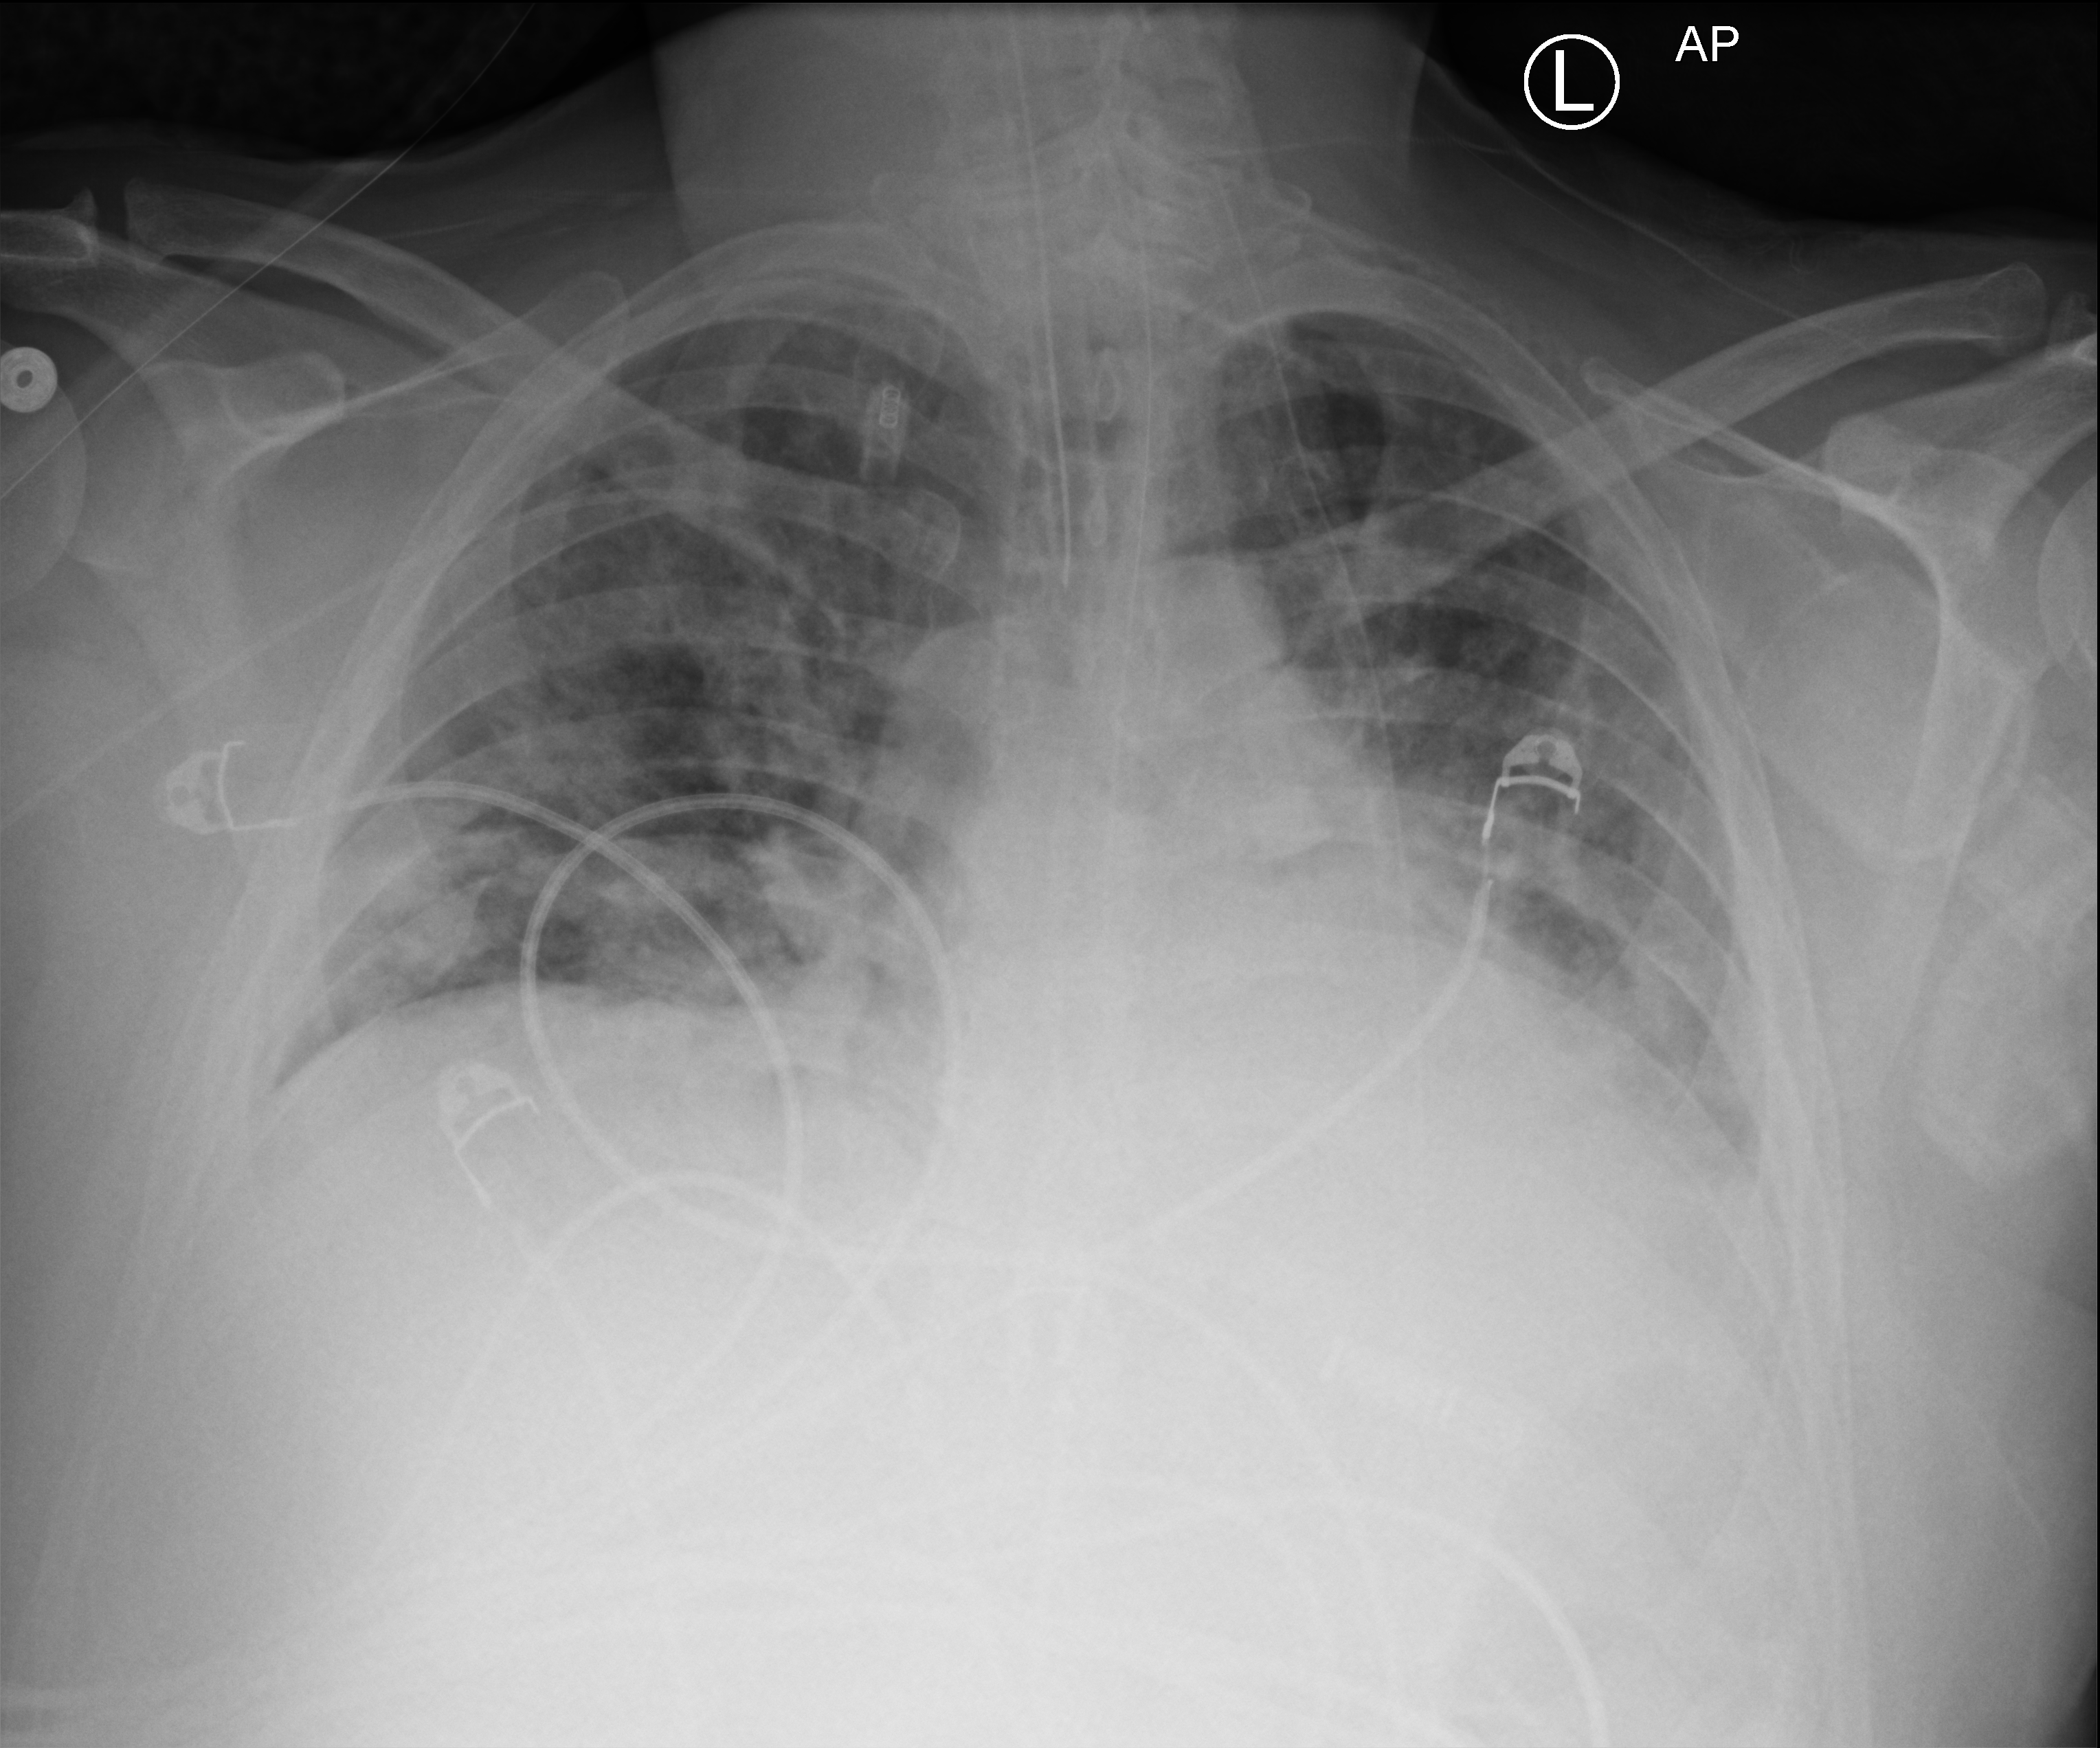
Bedside chest radiograph (computed radiography); anteroposterior (AP) projection. Patient hospitalised with COVID-19; male, aged 18–59 years.
Admission-level facts for this patient (not findings on this image; timing relative to this image not recorded):
- diabetes (admission record): no